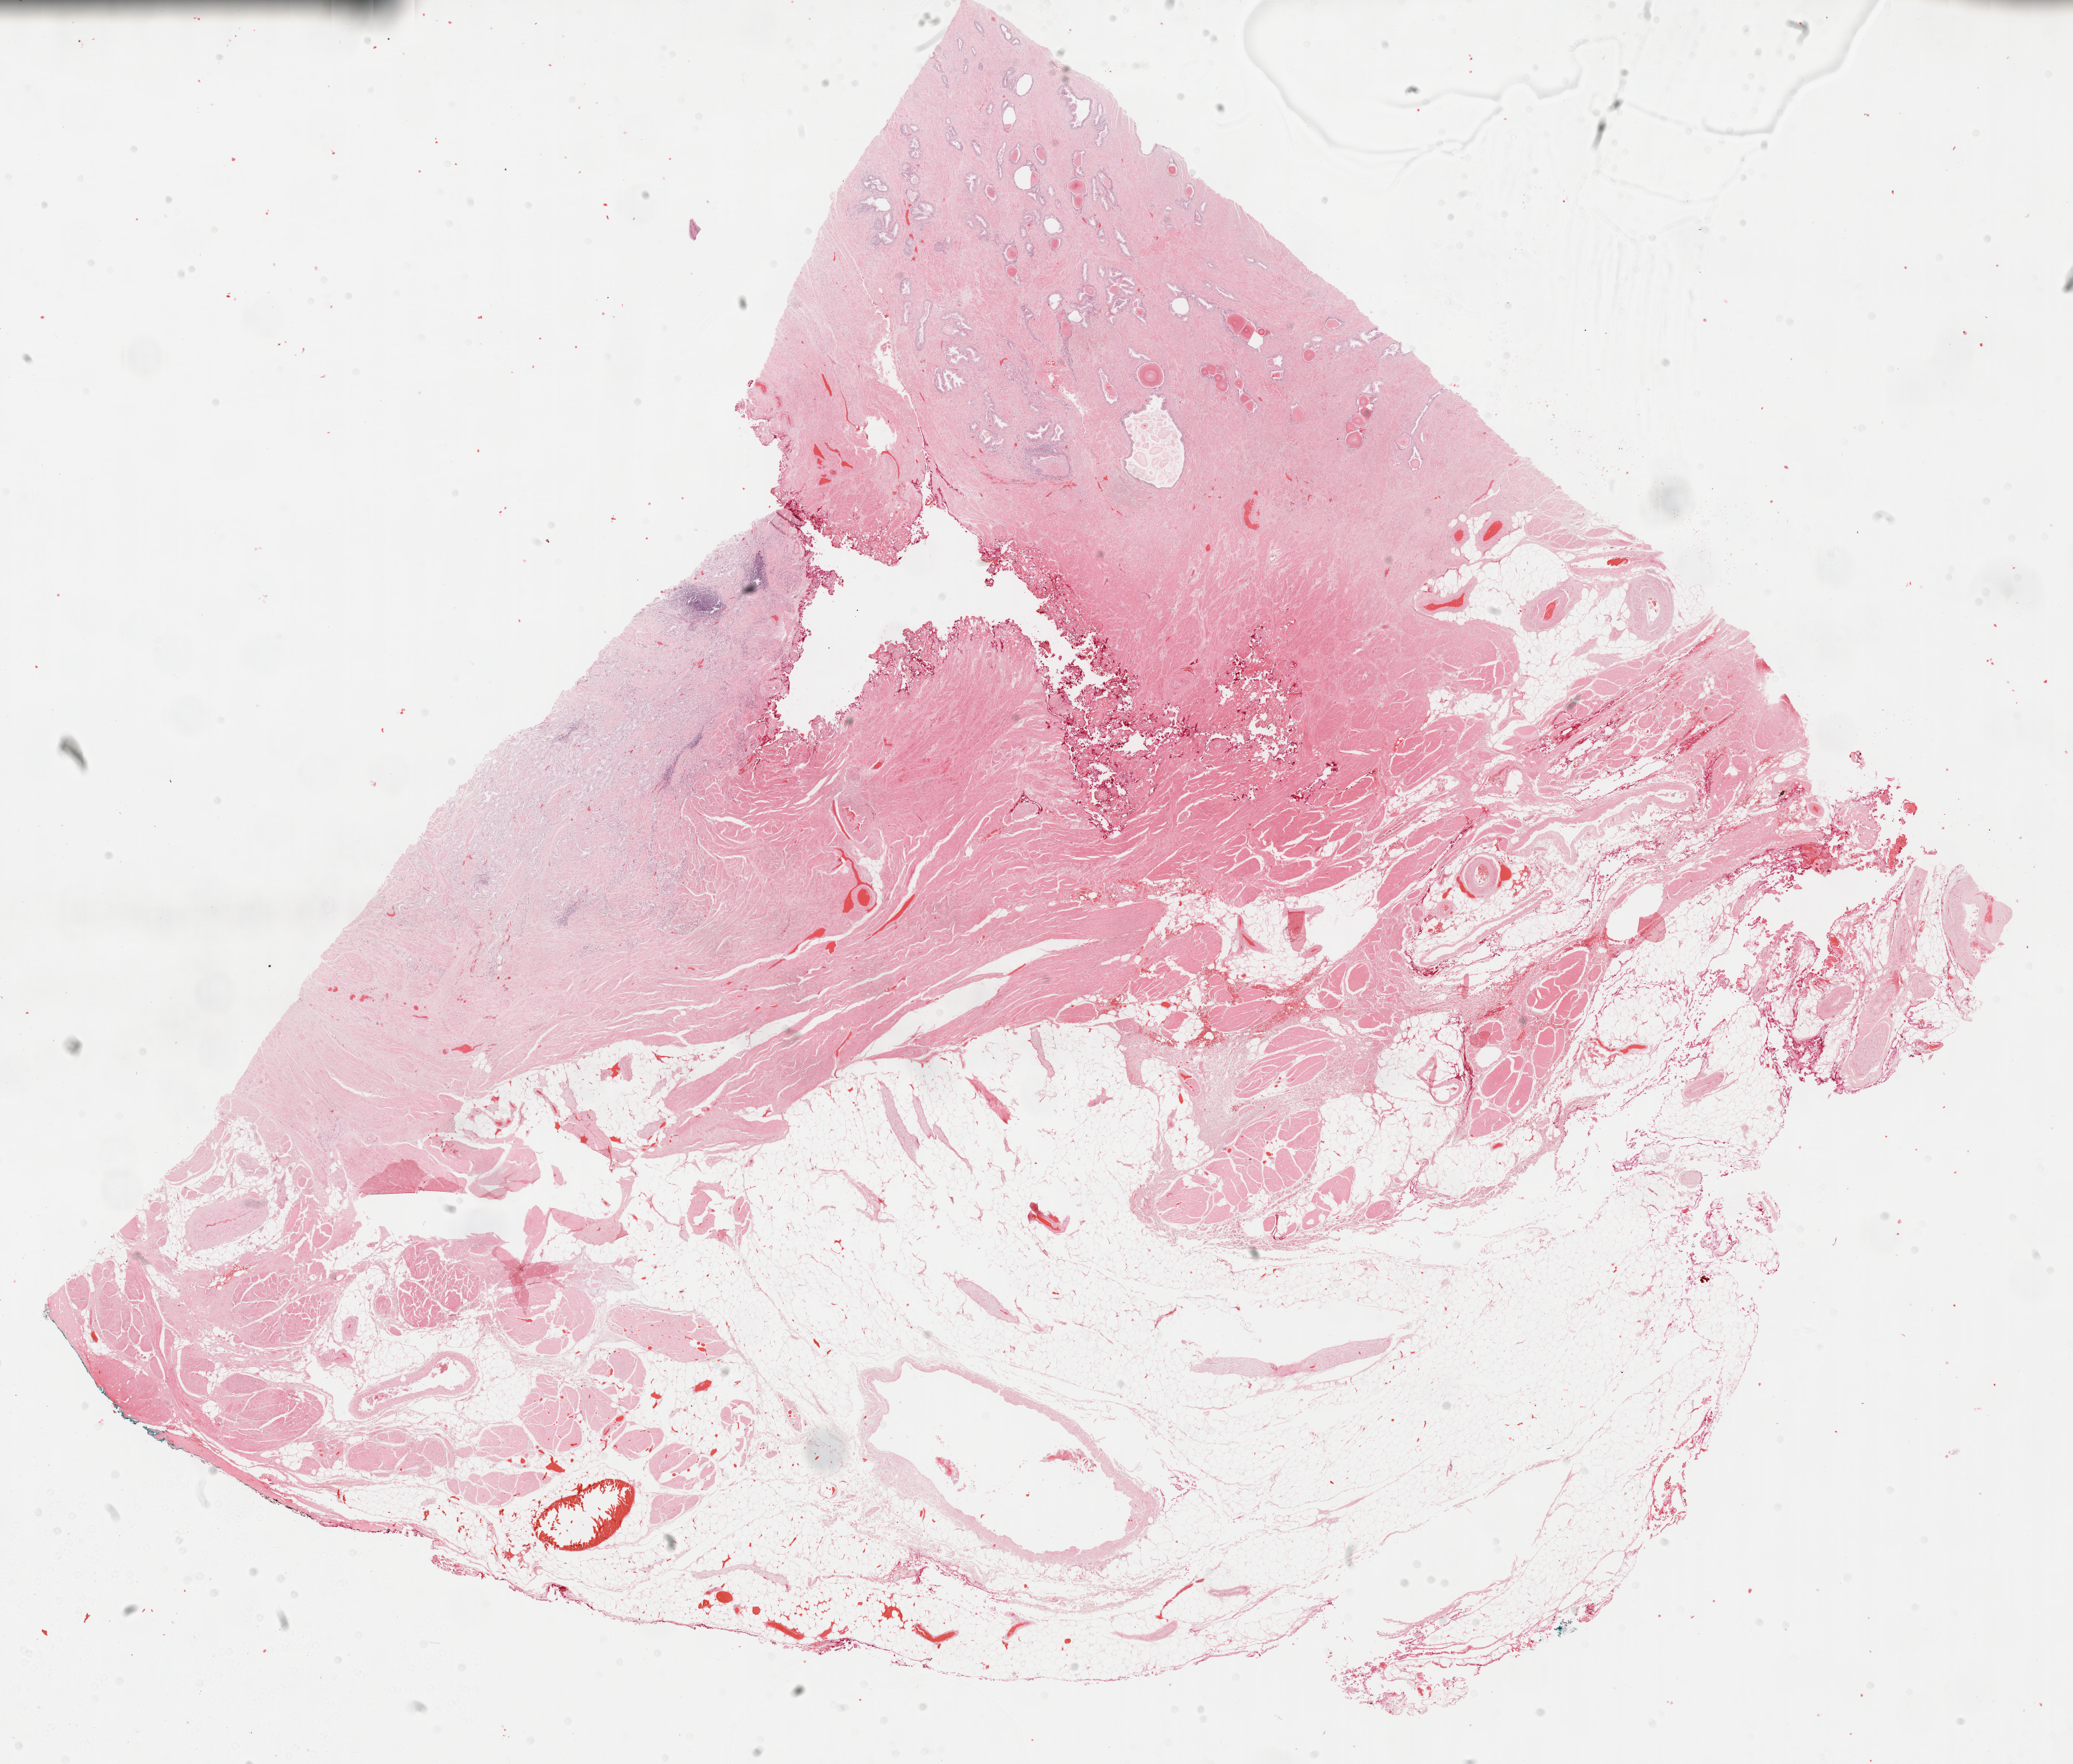
Digitized H&E tissue section (whole slide) — low-resolution overview of the scanned area, about 25.2 x 21.4 mm (from a 40x scan). FFPE section. Sample: primary tumour, prostate. Male, age 72 years at initial diagnosis. Gleason score: 8 (4+4).
Diagnosis: Adenocarcinoma, NOS. Lymph nodes positive (case pathology): 0 of 4 examined.